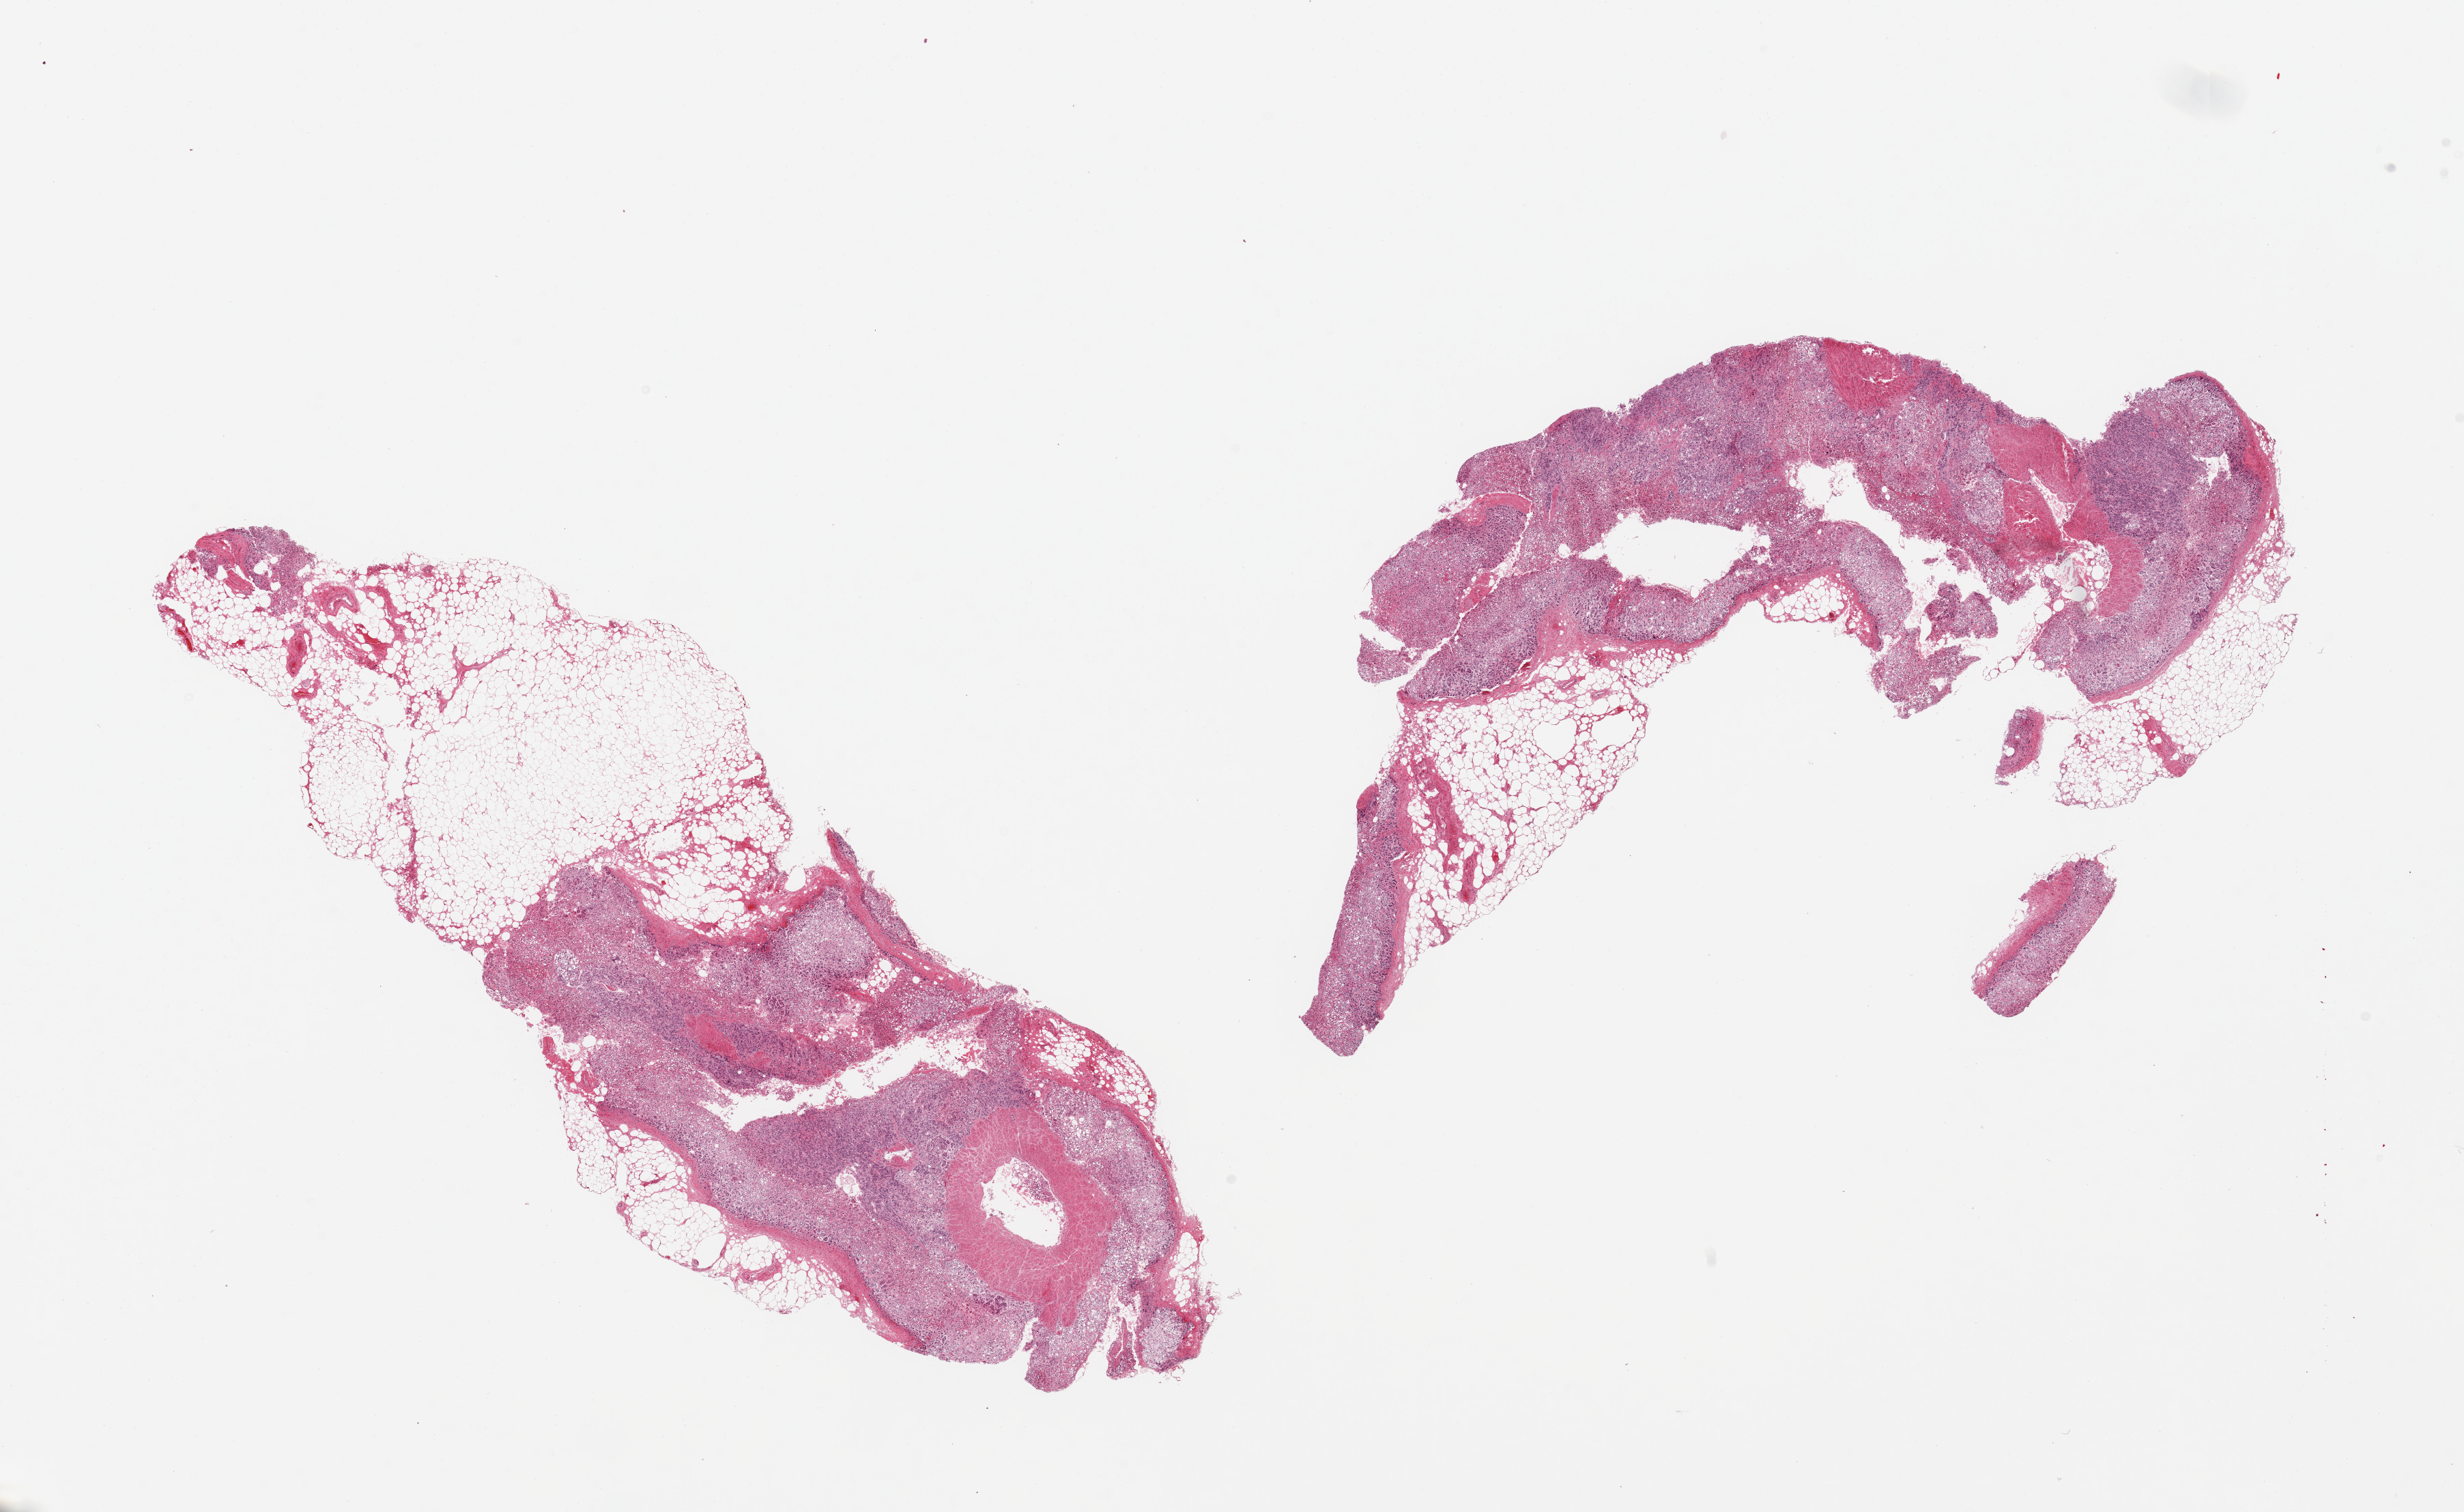
Whole-slide image, hematoxylin and eosin (H&E) stain, a low-resolution overview of the entire scanned area, about 28.5 x 17.5 mm (acquisition: 20x scan). PAXgene-fixed, paraffin-embedded tissue. Target tissue: adrenal gland. Tissue donor sample. Donor: female.
Pathologist's review note for this sample: 2 pieces, ~40% adherent fat, adrenal cortex, autolyzed.